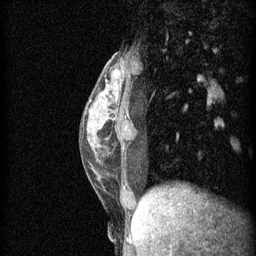
Breast MRI (dynamic contrast-enhanced), one sagittal slice. Position 21 of 60 along the scan axis. 3 images stored at this slice position (order not interpretable as contrast timing). 1.5 T. TE 4.2 ms, TR 11 ms. 2 mm slice thickness. 256 × 256 image matrix. Patient: female, 40 years.
Outlined on this slice (semi-automatically segmented with operator editing):
- analysis volume of interest (the breast-tissue region the enhancement analysis was run in; not a lesion): bounding box (x1, y1, x2, y2) in pixels: (80, 54, 167, 191)
- tumour enhancement mask (voxels above the 70 % enhancement threshold inside the analysis volume of interest): (114, 74, 117, 77)